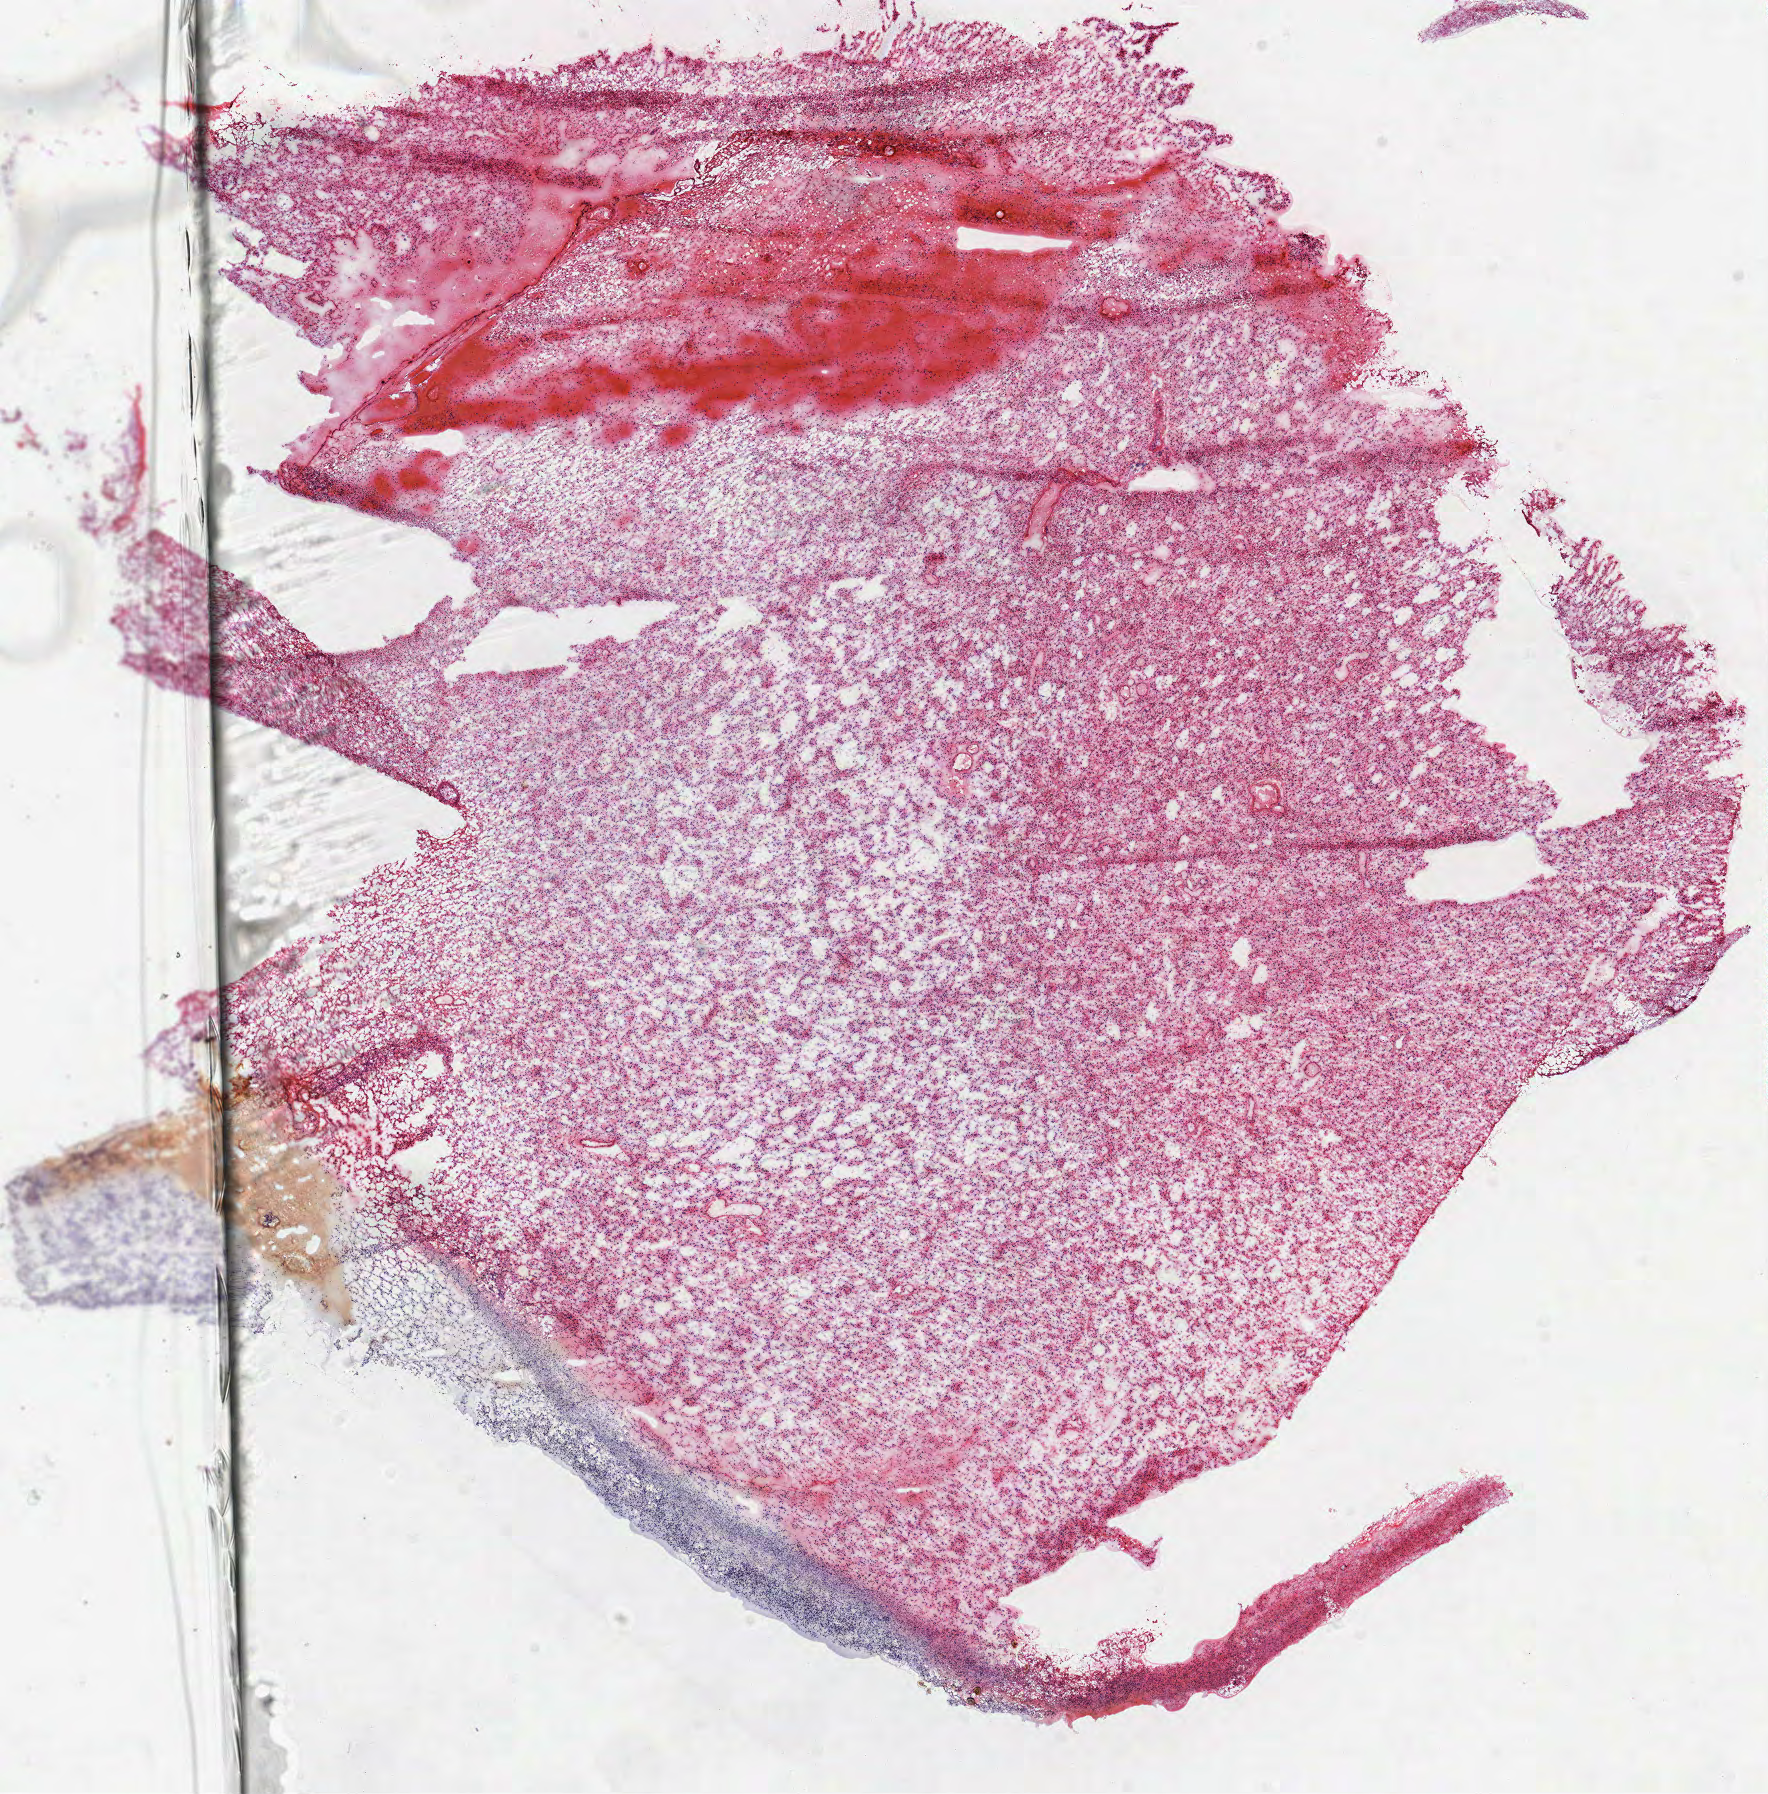
Digitized H&E tissue section (whole slide), whole scanned area (about 14.3 x 14.5 mm) shown as a low-resolution overview, frozen section from the top of the tissue portion, brain, primary tumour sample. Patient: male, age at initial diagnosis 41 years. Histologic grade: G2 (moderately differentiated). Pathologist review of this section (percent, as recorded): tumour cells 100%, tumour nuclei 85%, normal cells 0%, stromal cells 0%, necrosis 0%.
Pathologic diagnosis: Astrocytoma, NOS (cerebrum).